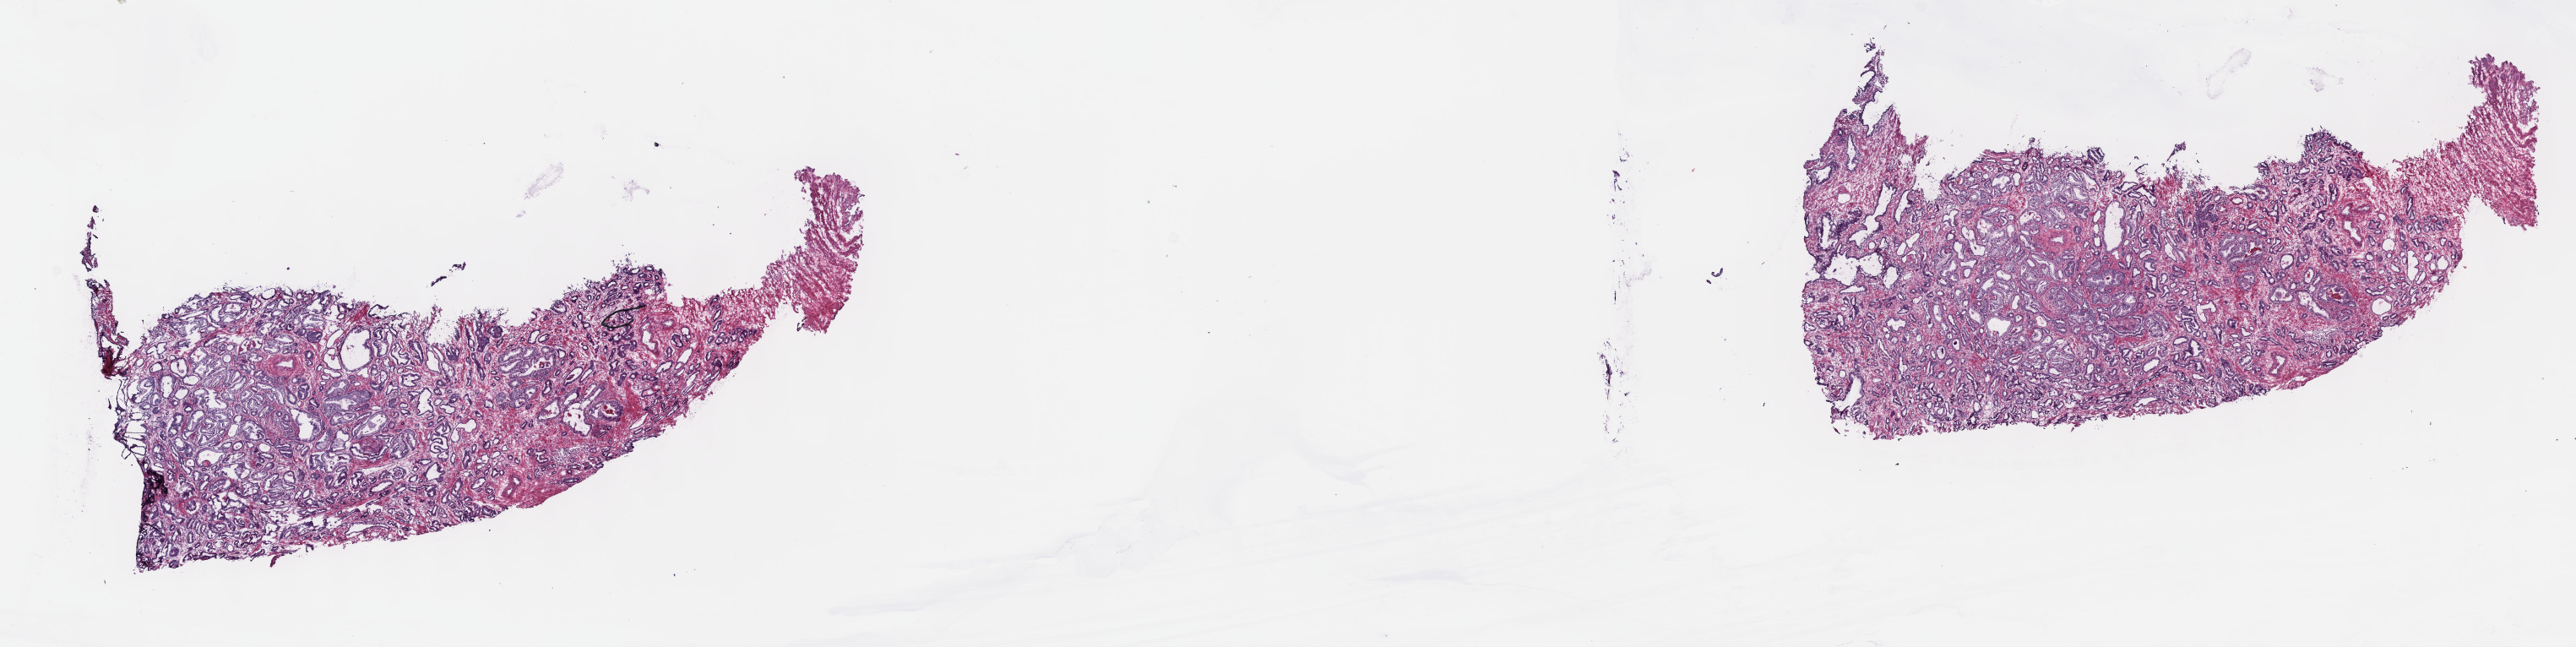
Digitized Hematoxylin and eosin (H&E) stained tissue section (whole slide) — low-resolution overview of the scanned area, about 24.7 x 6.2 mm (from a 40x scan), frozen section, sample: primary tumour, prostate. Male, age 52 years at initial diagnosis.
Histologic diagnosis: Adenocarcinoma, NOS (prostate gland).